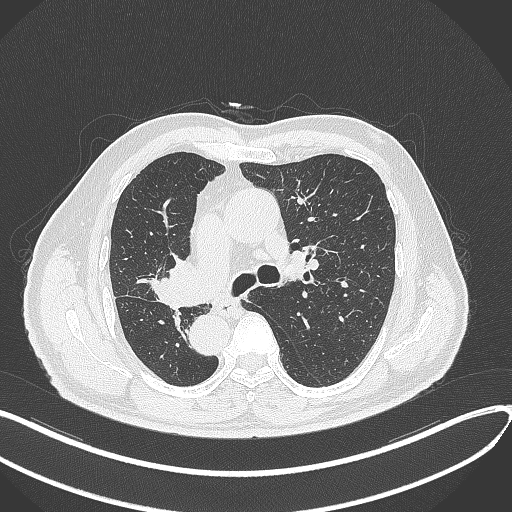
Chest CT, one axial slice; position 188 of 300 along the scan axis; reconstruction kernel B70f; lung window (W 1500 / L -600 HU); 1 mm slice thickness; 512 × 512 image matrix, field of view 400 × 400 mm. Male patient, age 67 years. From the clinical record (not read from this slice): clinical TNM (as recorded): T2a N0 M0.
Annotated regions visible in this slice (rectangle marked by the reading radiologist):
- lung tumour (recorded histology: squamous cell carcinoma): bounding box [x1, y1, x2, y2] px = [148, 249, 197, 310]